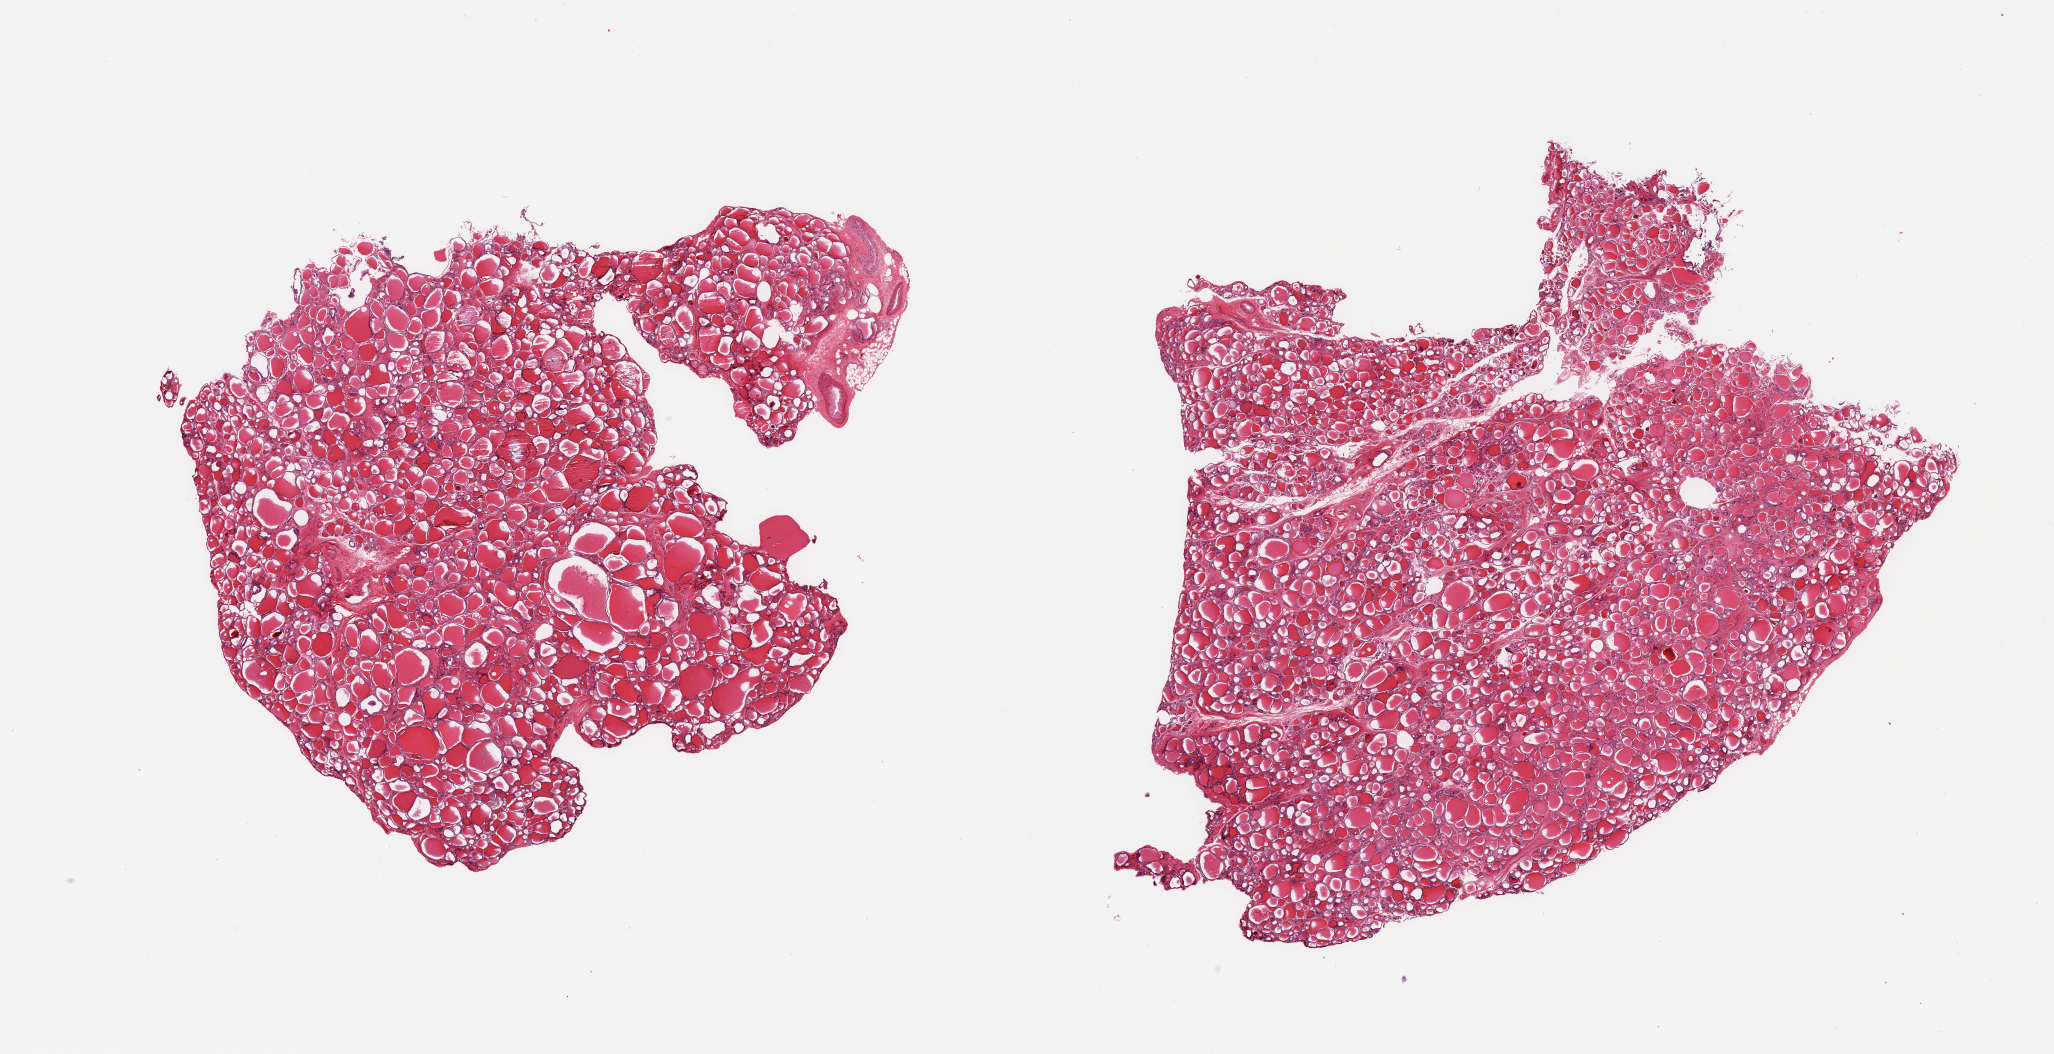
H&E whole-slide image, a low-resolution overview of the entire scanned area, about 32.5 x 16.7 mm; PAXgene-fixed, paraffin-embedded tissue; sampled site (target tissue): thyroid; donor tissue sample. Donor sex: female.
• reviewer comment on this tissue sample: 2 pieces; no lesions